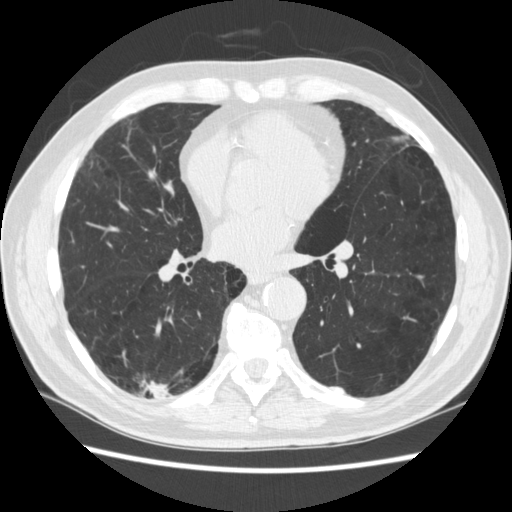
Low-dose screening chest CT, one axial slice; position 124 of 266 along the scan axis; reconstruction kernel STANDARD; 120 kVp; lung window (W 1500 / L -600 HU); 1.25 mm slice thickness; 512 × 512 image matrix, field of view 360 × 360 mm.
Annotated regions visible in this slice (expert manual segmentation):
- lesion 1 (tumor, upper lobe of right lung): box from (x=149, y=383) to (x=168, y=399) px